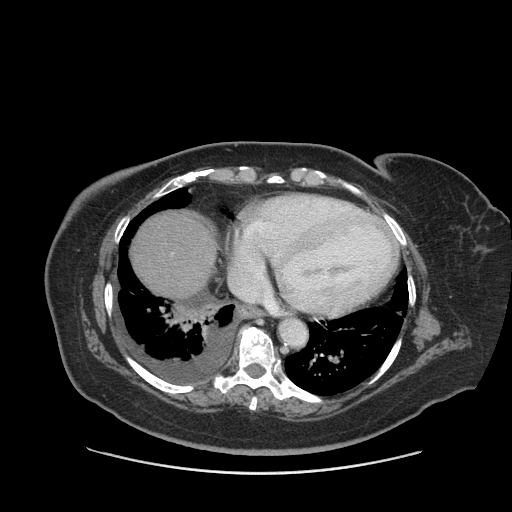
Contrast-enhanced abdominal CT (liver protocol), one axial slice; position 81 of 91 along the scan axis; reconstruction kernel STANDARD; 140 kVp; soft-tissue window (W 400 / L 40 HU); 2.5 mm slice thickness; 512 × 512 image matrix. Case-level facts recorded for this patient, not image findings: diagnosis: hepatocellular carcinoma (patient treated with transarterial chemoembolisation; whether this scan precedes or follows treatment is not stated here); TNM stage (as recorded): Stage-I; Child-Pugh class: A; tumour differentiation: well differentiated; tumour nodularity: uninodular.
Annotated regions visible in this slice (semi-automatically segmented with operator editing):
- abdominal aorta: bounding box <280,319,306,345> (left, top, right, bottom; pixels)
- liver parenchyma outside the tumour (the mass and vessels are separate outlines, so this box may not span the whole liver): <130,210,216,296>